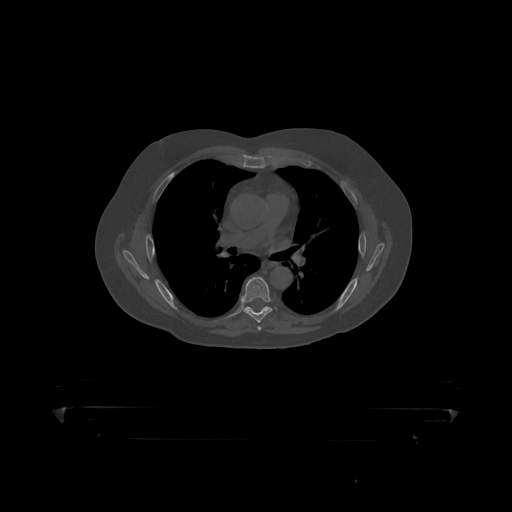
CT including the spine, one axial slice. Position 297 of 390 along the scan axis. 120 kVp. Bone window (W 1800 / L 400 HU). 1.25 mm slice thickness. 512 × 512 image matrix, field of view 650 × 650 mm. Male patient, age 60 years. From the clinical record (not read from this slice): primary cancer: prostate.
Structures marked on this image (semi-automatic segmentation, software-assisted and operator-edited):
- T6 vertebra: bounding box <241,277,273,319> (left, top, right, bottom; pixels)
- T7 vertebra: <246,307,270,311>